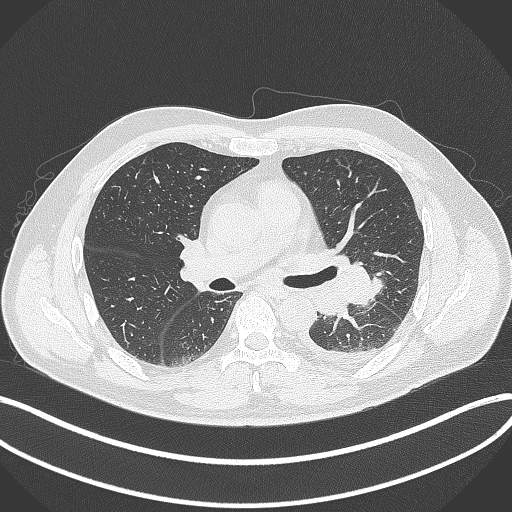
Chest CT, one axial slice. Slice 207 of 342 in the series (ordered by position). Reconstruction kernel B70f. Lung window (W 1500 / L -600 HU). 1 mm slice thickness. 512 × 512 image matrix, field of view 400 × 400 mm. Patient: male, 58 years. Case-level facts recorded for this patient, not image findings: clinical TNM (as recorded): T3 N1 M1b.
Structures marked on this image (bounding box drawn by a radiologist):
- lung tumour (recorded histology: small cell carcinoma): bounding box <344,259,384,307> (left, top, right, bottom; pixels)